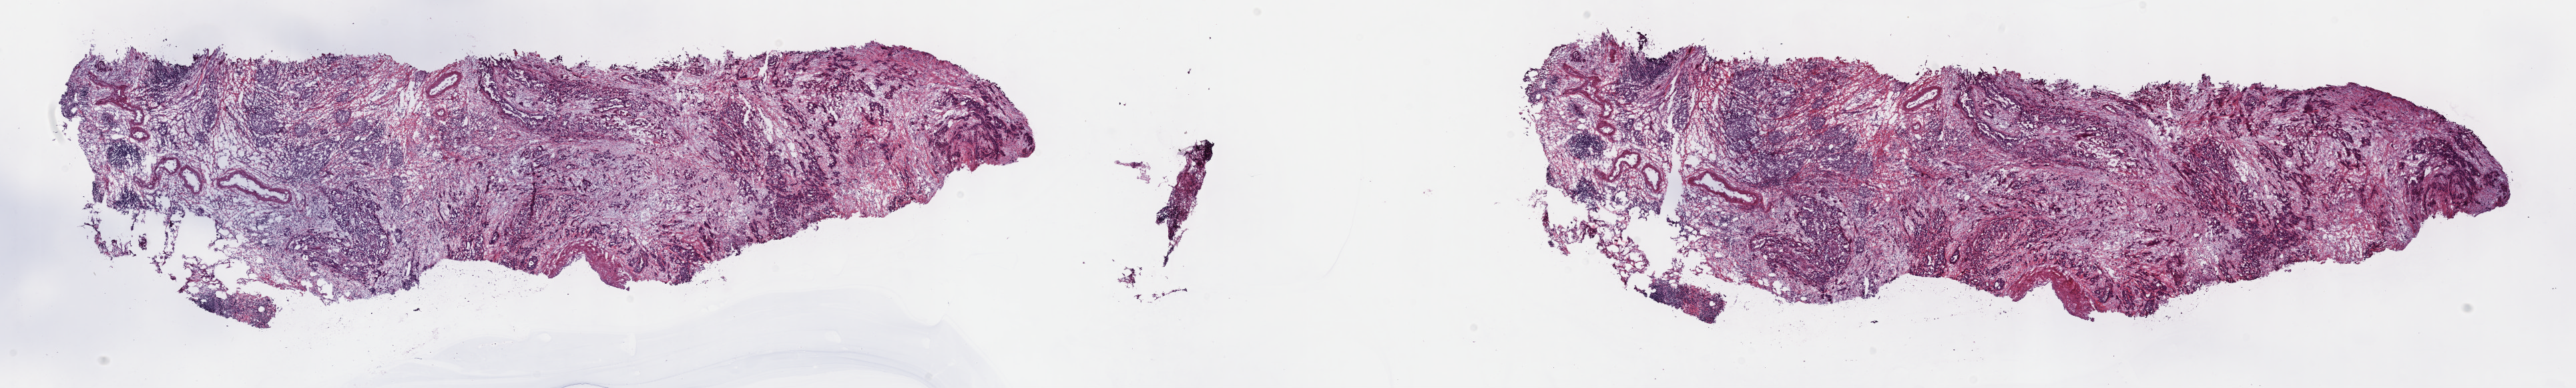
Whole-slide histology image, H&E-stained — whole scanned area (about 31.2 x 4.7 mm) shown as a low-resolution overview. Frozen section from the top of the tissue portion. Pancreas, primary tumour sample. Patient: female, age at initial diagnosis 80 years. Histologic grade: G3 (poorly differentiated). Composition of this section per pathologist review: tumour cells 27%, tumour nuclei 70%, normal cells 10%, stromal cells 58%, necrosis 5%. Infiltration values recorded for this section: lymphocyte infiltration 25%, monocyte infiltration 1%, neutrophil infiltration 1%.
* AJCC pathologic stage: IIB (7th edition)
* lymph nodes positive (case pathology): 2 of 23 examined
* pathologic diagnosis: Infiltrating duct carcinoma, NOS (head of pancreas)